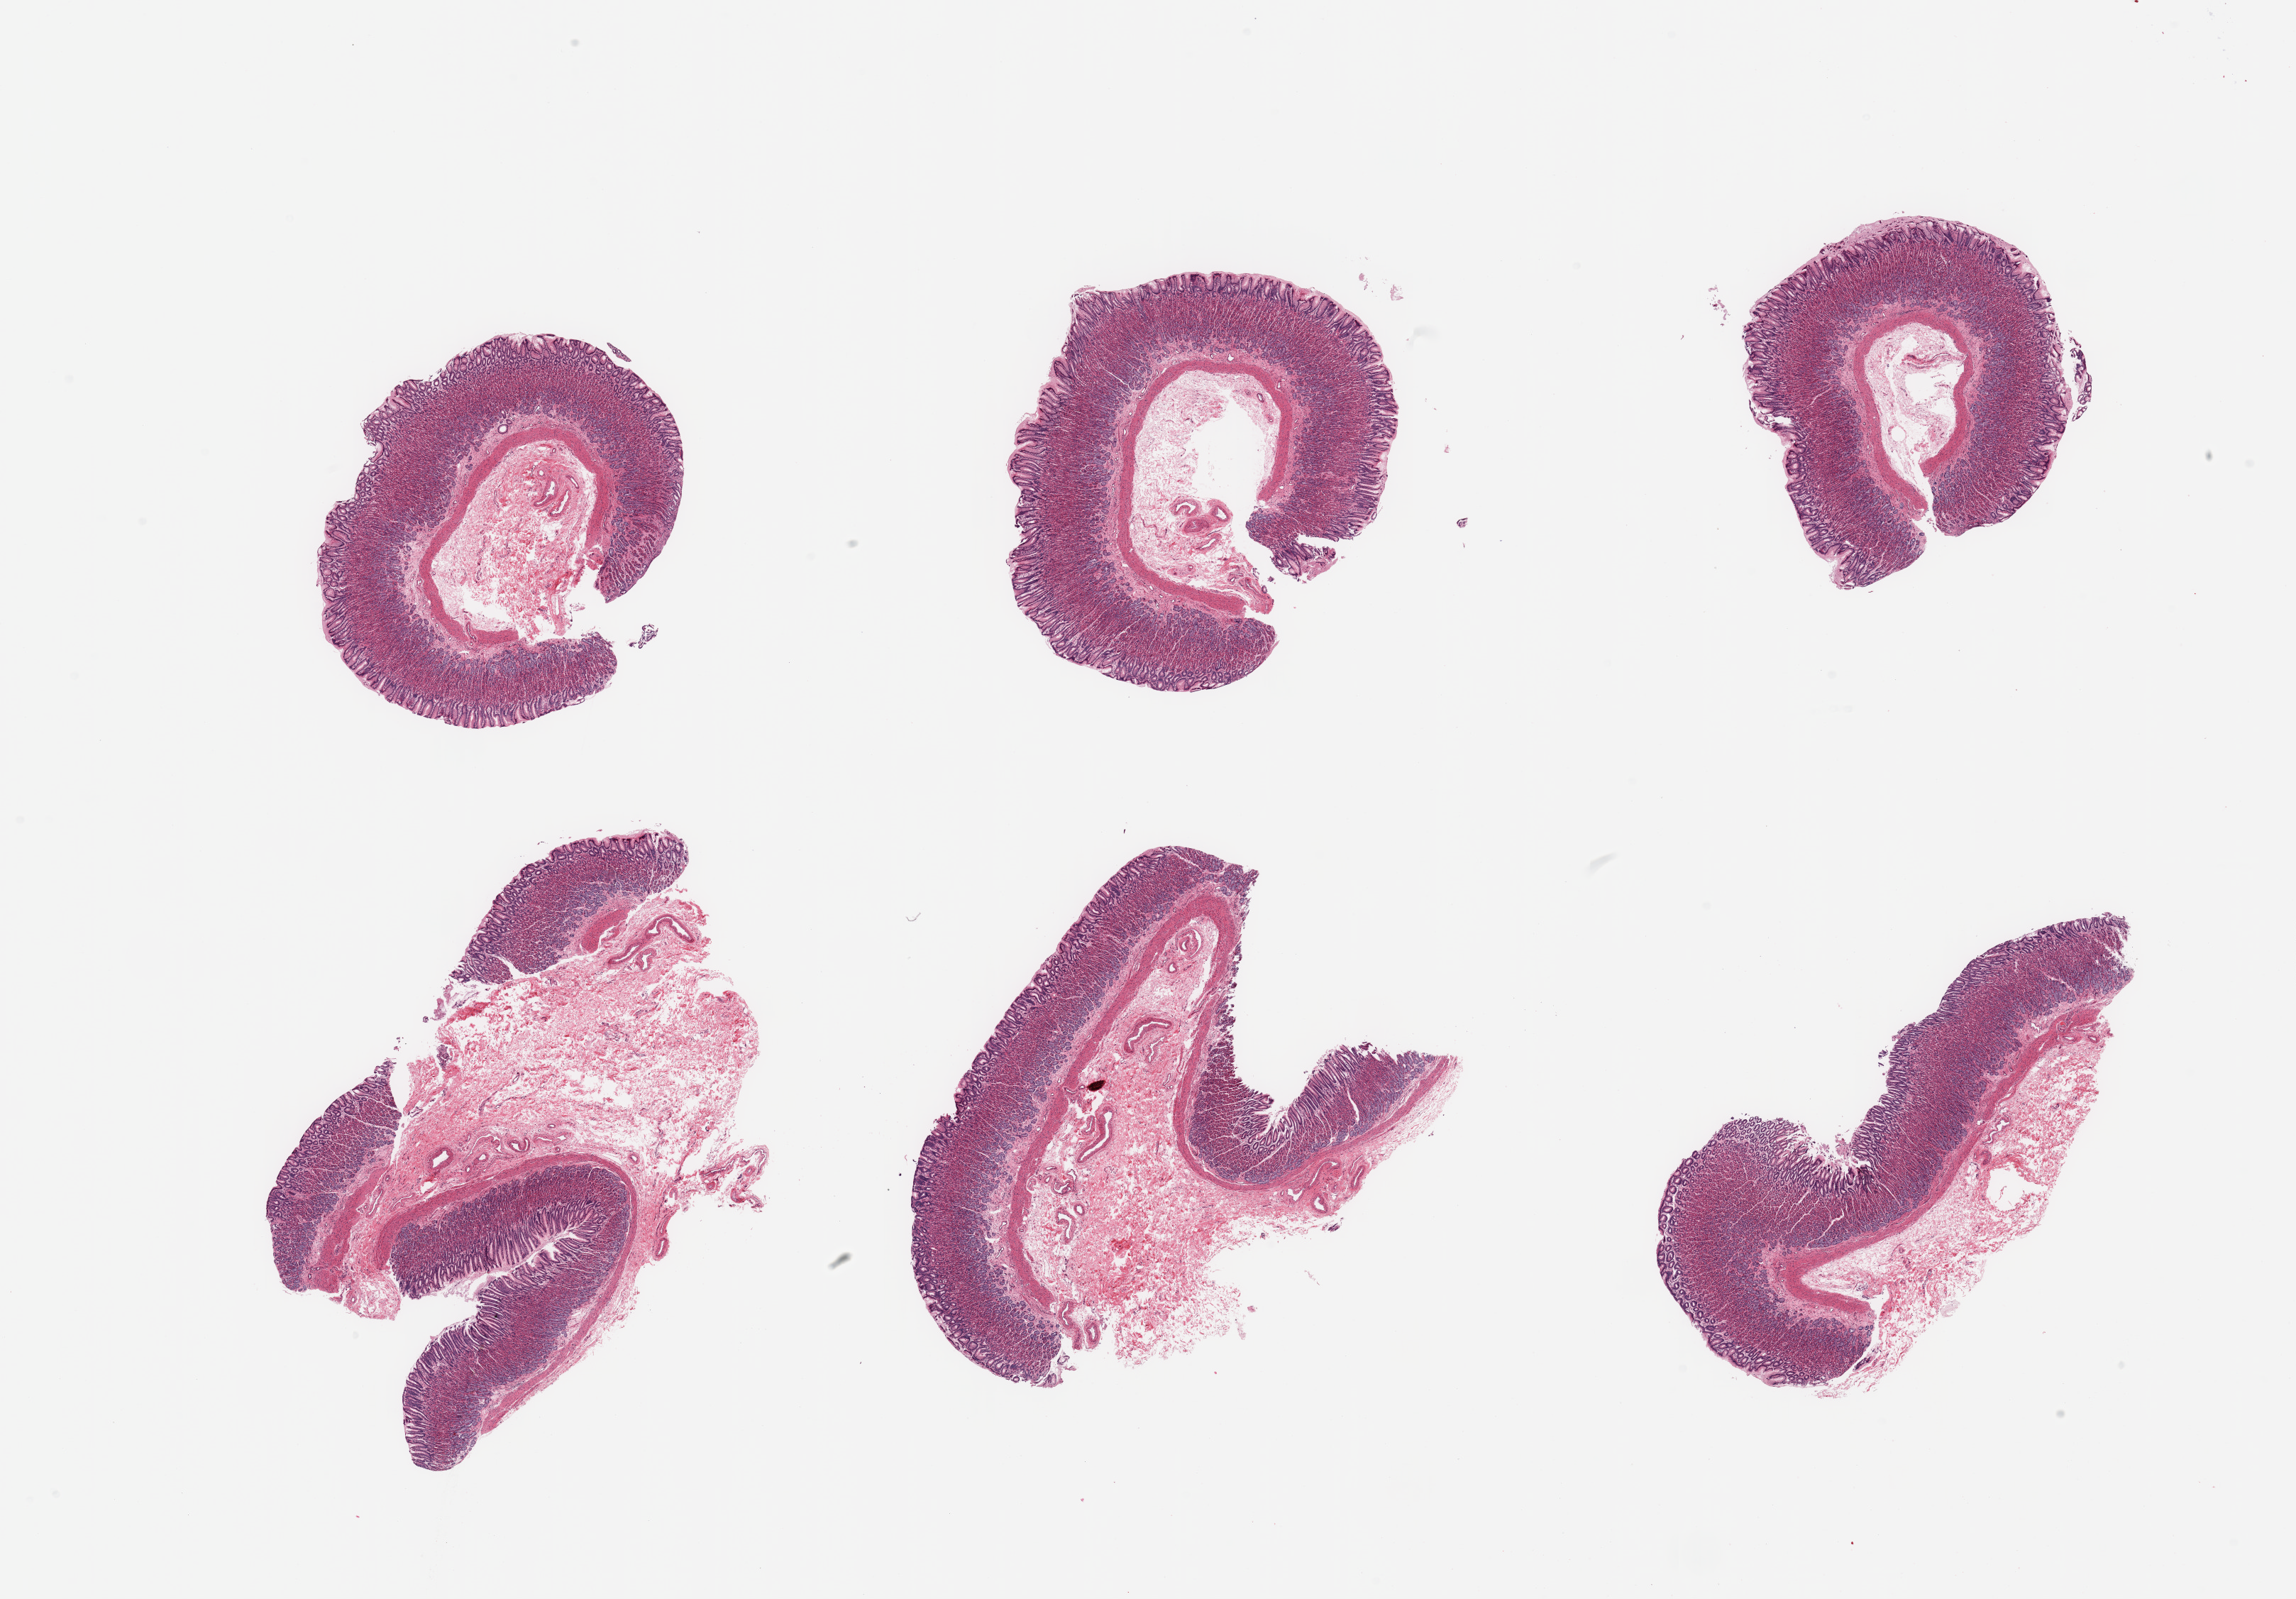
Whole-slide image, H&E stain, whole scanned area (about 25.6 x 17.8 mm, slide scanned at 20x) shown as a low-resolution overview; PAXgene-fixed paraffin-embedded (PFPE) section; section of stomach (target tissue); donor tissue sample. Donor: female.
Review note (as recorded): 6 pieces, mucosa well fixed, up to 1.2mm, 40-50% thickness.